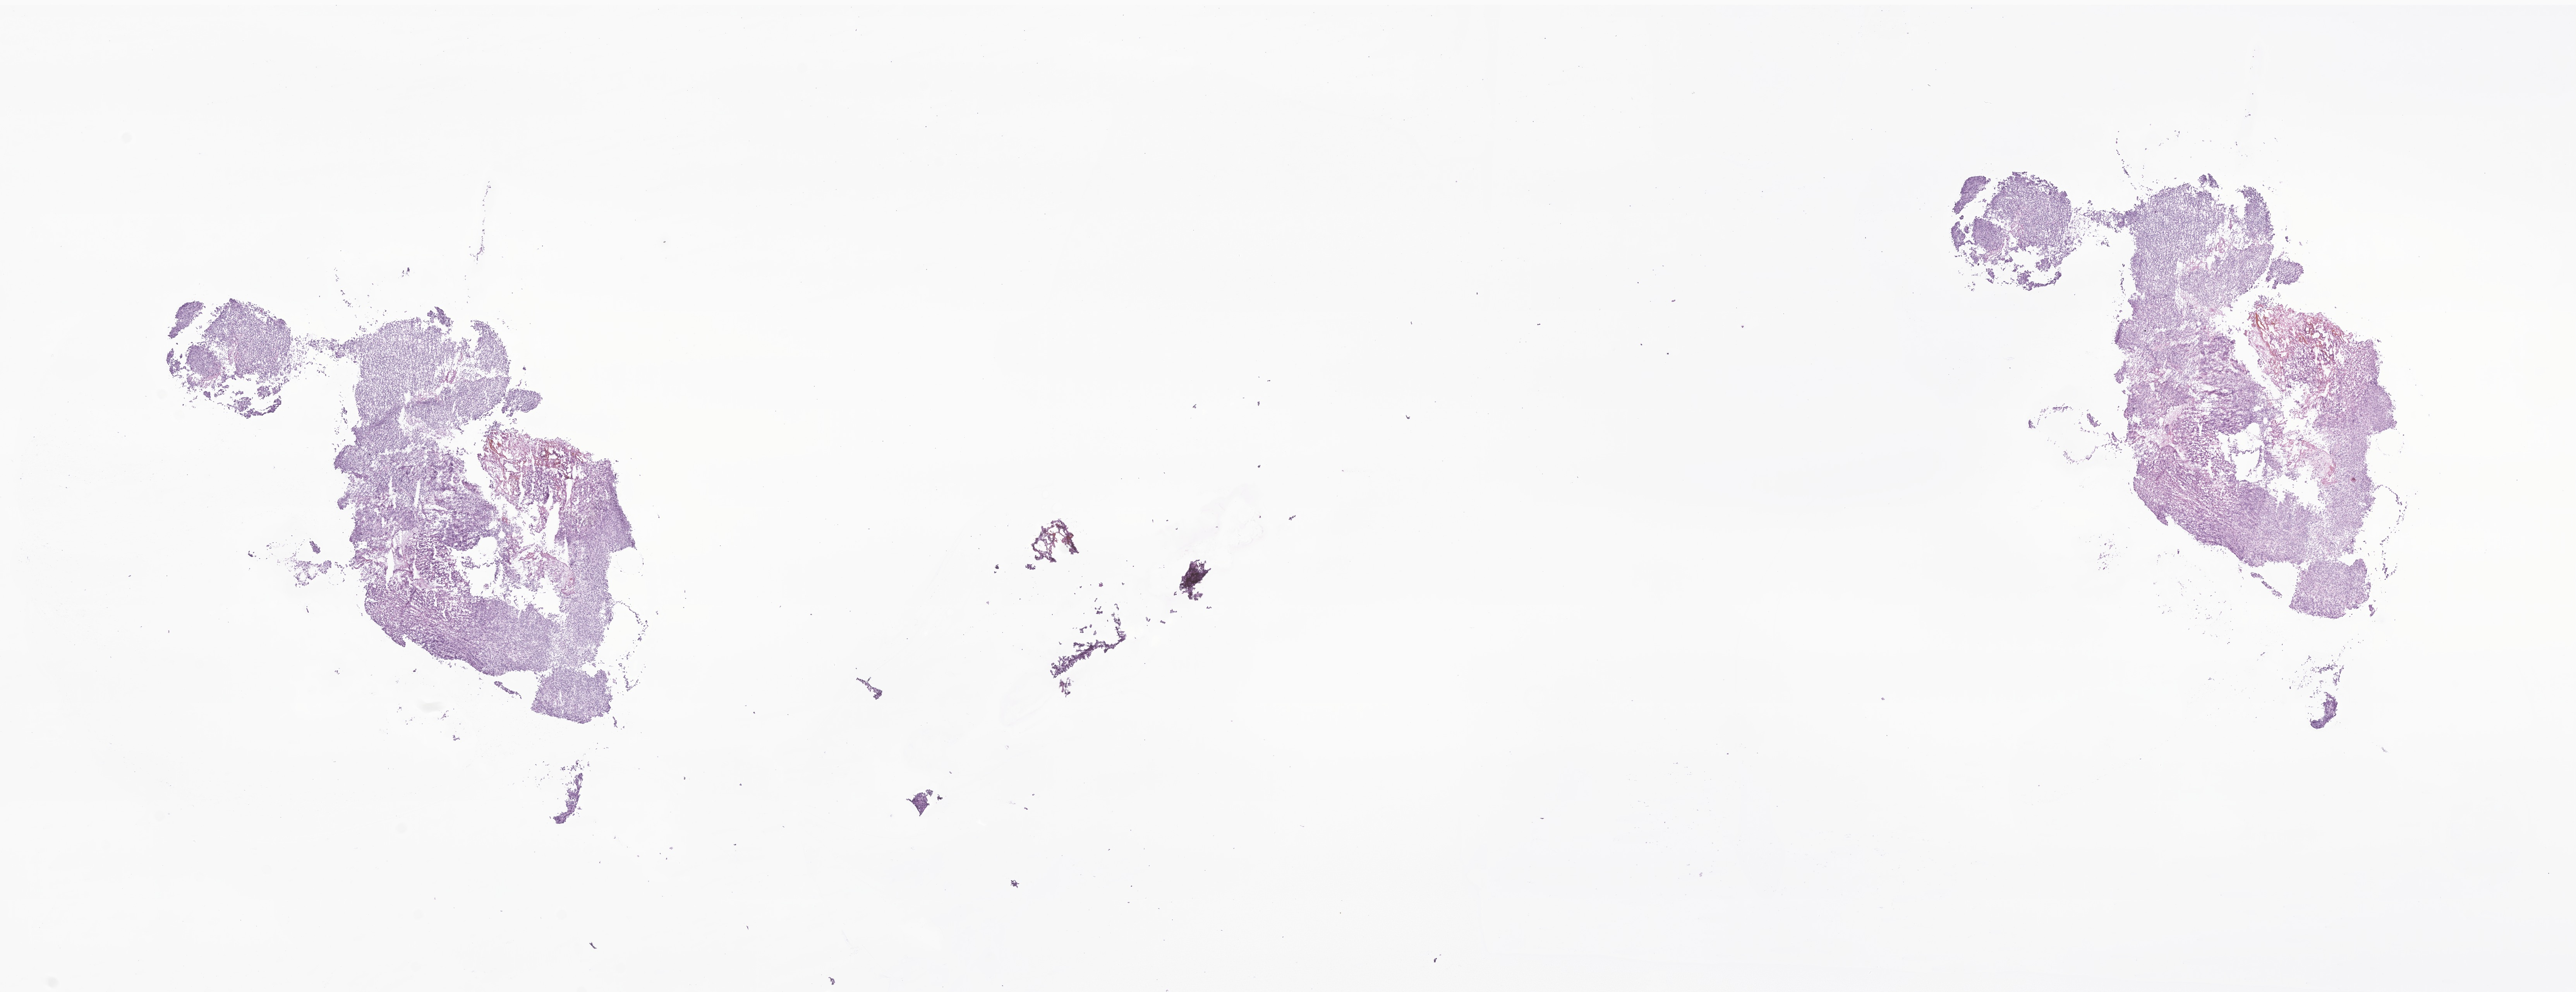
Whole-slide image, H&E stain of tumor tissue from the brain — low-resolution overview of the scanned area, about 28.0 x 10.8 mm. Frozen section. Patient: female, age 91 months (7 years 7 months).
- diagnosis: Atypical teratoid/rhabdoid tumor